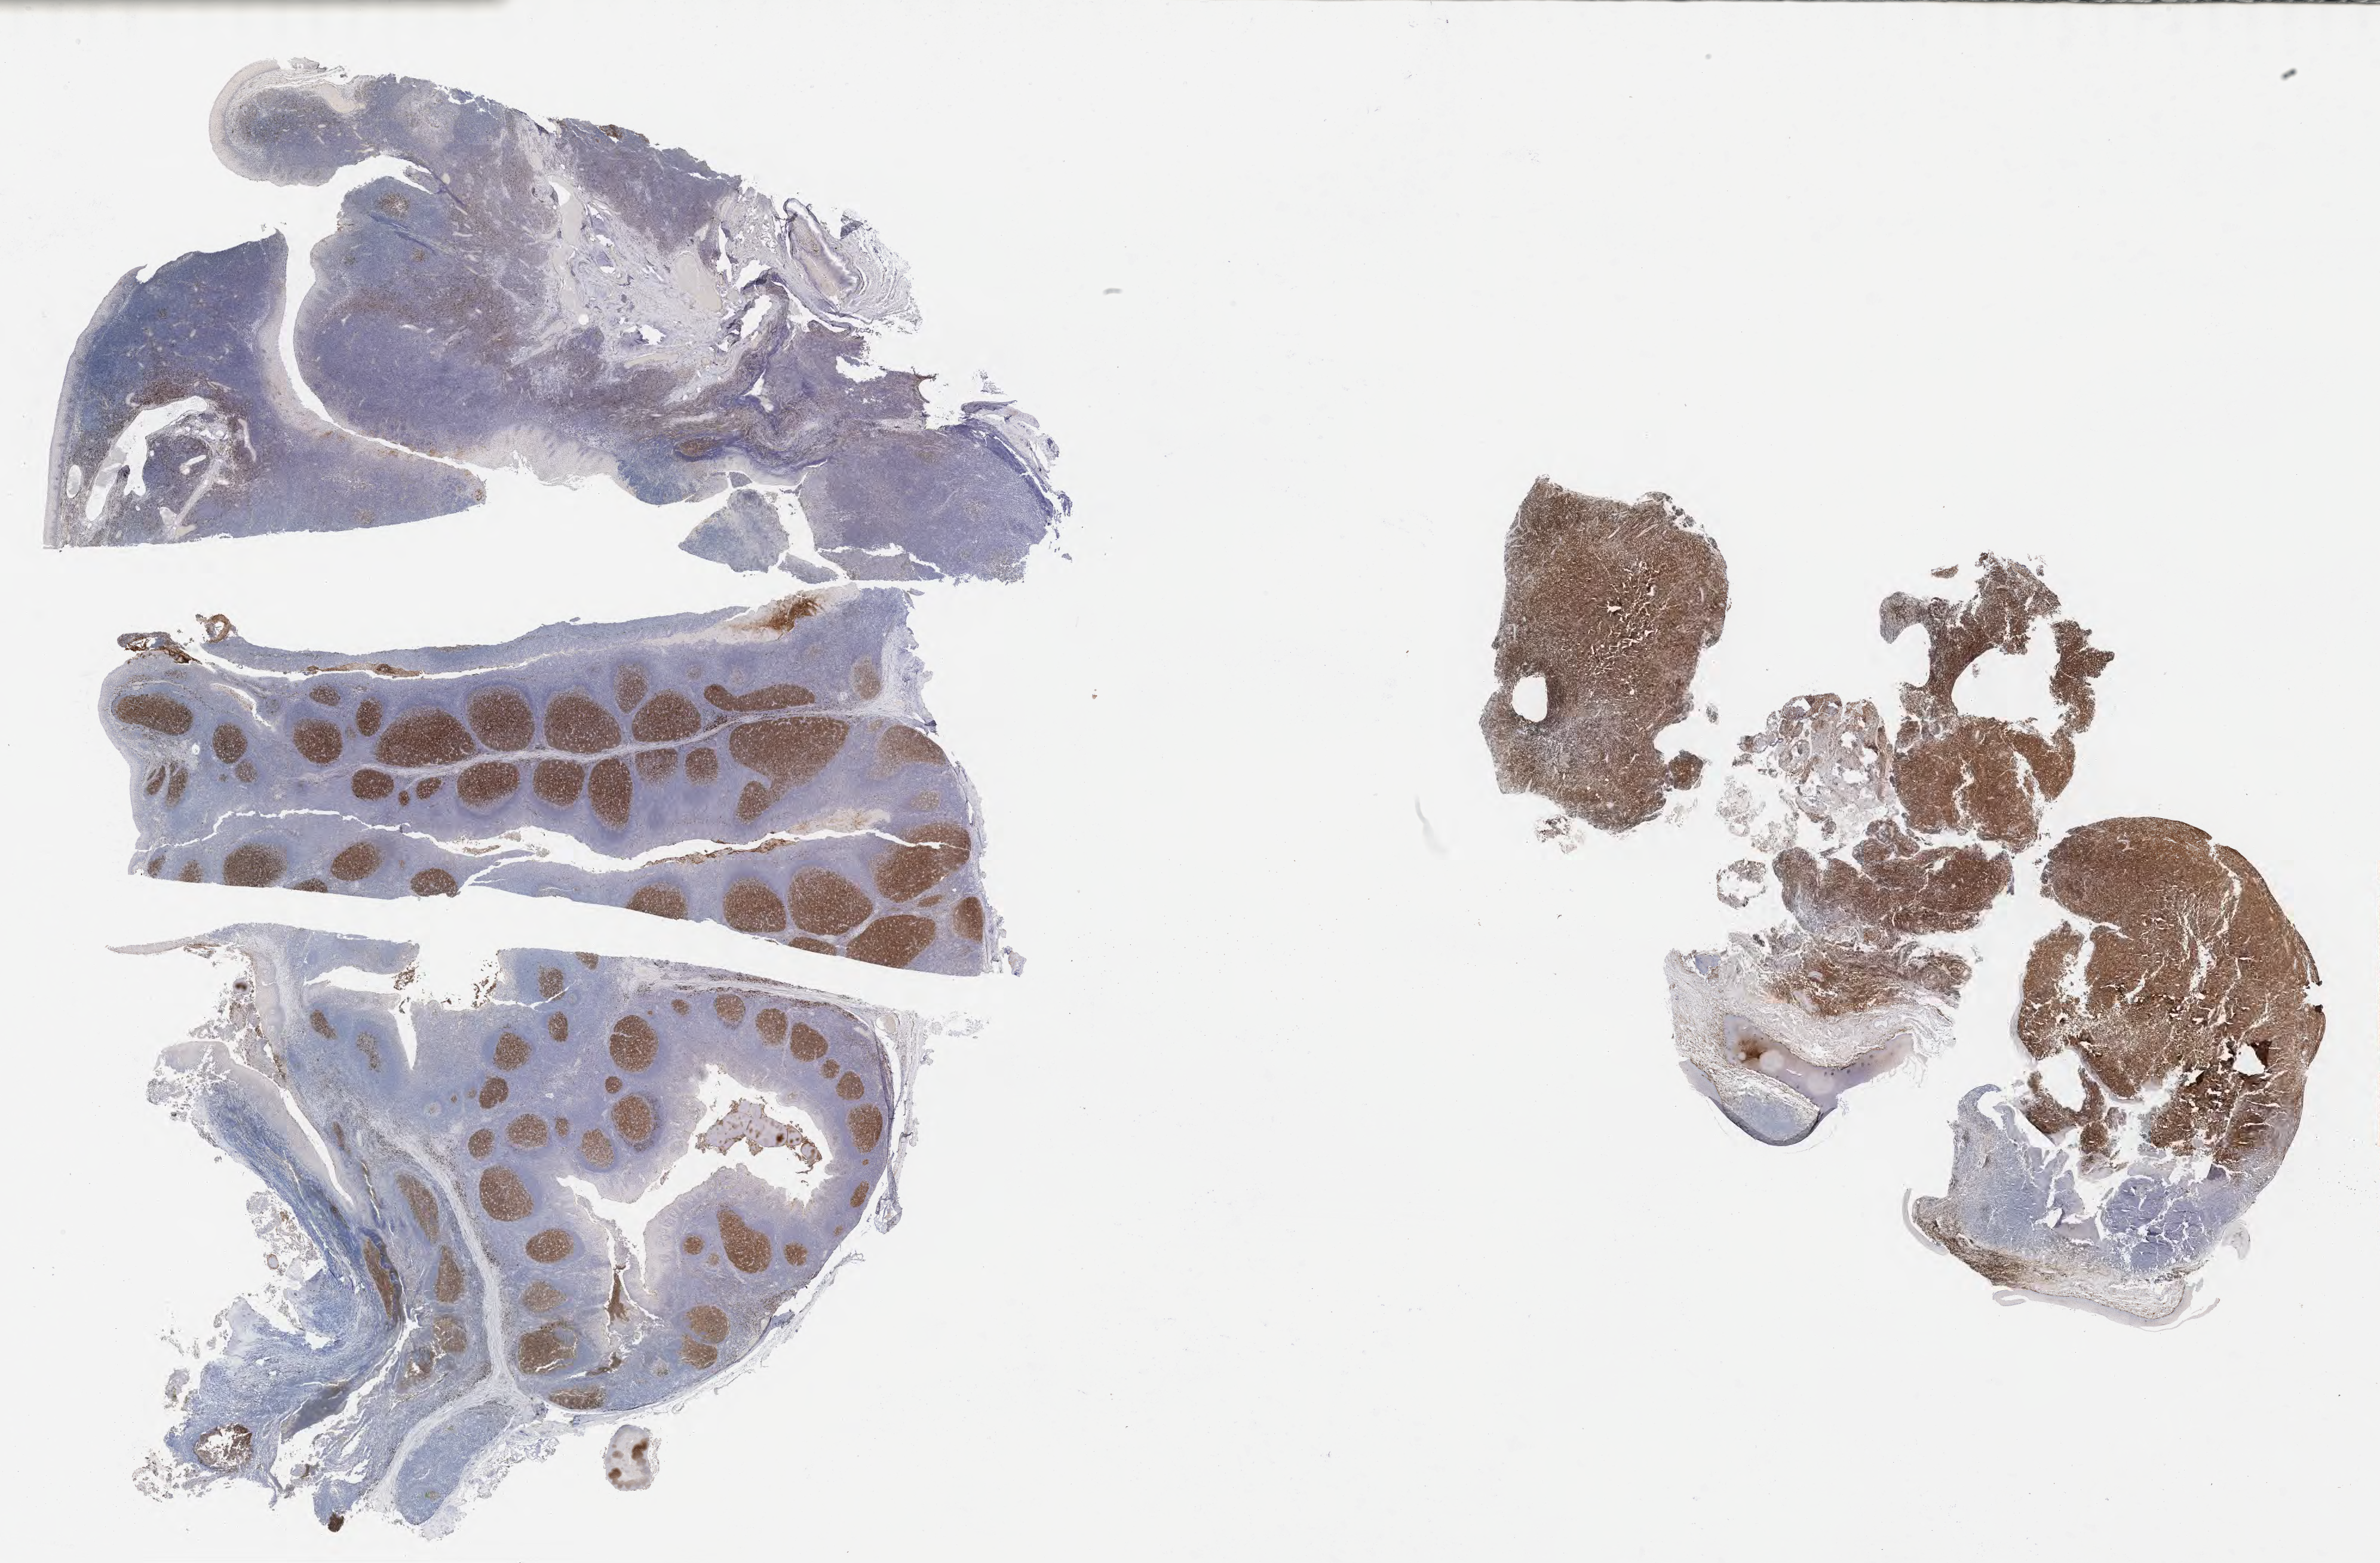
Immunohistochemistry (IHC) whole-slide image stained for CD10, shown as a low-resolution overview of the whole scanned area (about 32.2 x 21.1 mm). Specimen: tumor tissue. Male patient, 63 years old.
Histologic diagnosis: Burkitt lymphoma, NOS.